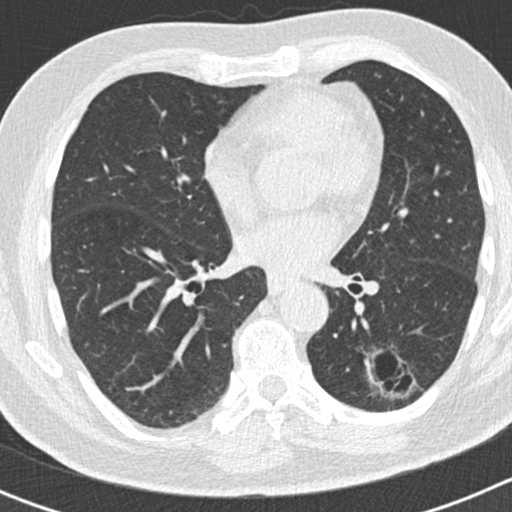
Low-dose screening chest CT, axial slice; second annual screen; lung window (W 1500 / L -600 HU); 2 mm slice thickness; 120 kVp; slice 91 of 186 in the series; 512 × 512 image matrix. Male participant, aged 66 years at enrolment.
Expert-annotated lung lesion, bounding box (x1, y1, x2, y2) in pixels: (350, 335, 413, 406). Screening reader's record for this exam (one nodule recorded; not confirmed to be the boxed lesion): non-calcified nodule or mass ≥4 mm, left lower lobe, 50 × 33 mm, smooth margins, pre-existing on the prior screen: yes; interval growth: yes. Official screen result: positive, other. Later outcome: lung cancer diagnosed 440 days after this screen — adenocarcinoma, NOS, left lower lobe, poorly differentiated (G3), stage IB (AJCC 6th edition), 38 mm at pathology.